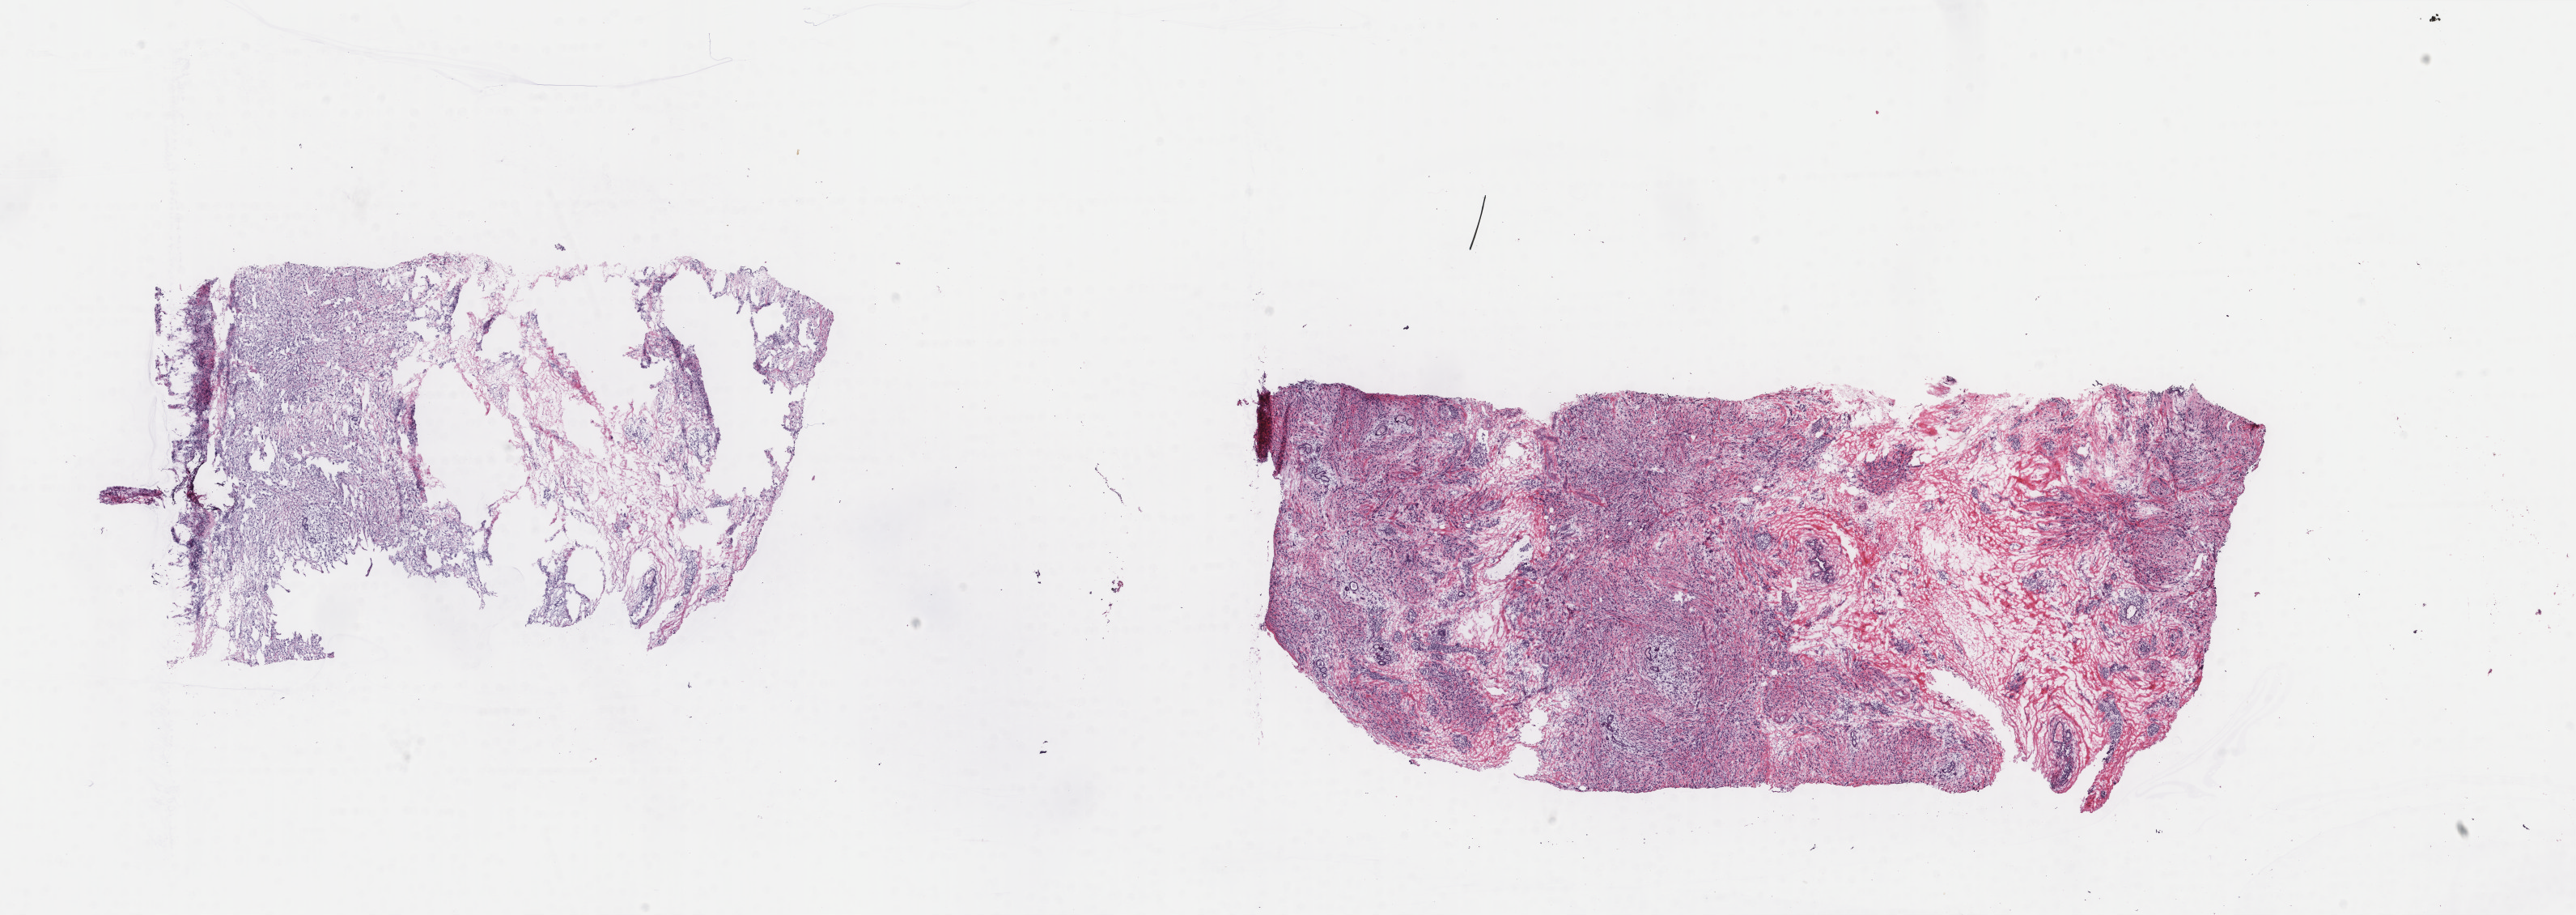
H&E-stained whole-slide image, whole scanned area (about 25.3 x 9.0 mm, acquisition: 40x scan) shown as a low-resolution overview; frozen section from the top of the tissue portion; primary tumour sample from the breast. Female, age 60 years at initial diagnosis. Pathologist review of this section (percent, as recorded): tumour cells 85%, tumour nuclei 80%, normal cells 5%, stromal cells 10%, necrosis 0%. Inflammatory infiltration, as recorded: lymphocyte infiltration 0%, monocyte infiltration 0%, neutrophil infiltration 0%.
• histologic diagnosis: Lobular carcinoma, NOS
• lymph nodes positive (case pathology): 3 of 15 examined
• TNM: T3 N1 M0
• AJCC pathologic stage: IIIA (6th edition)